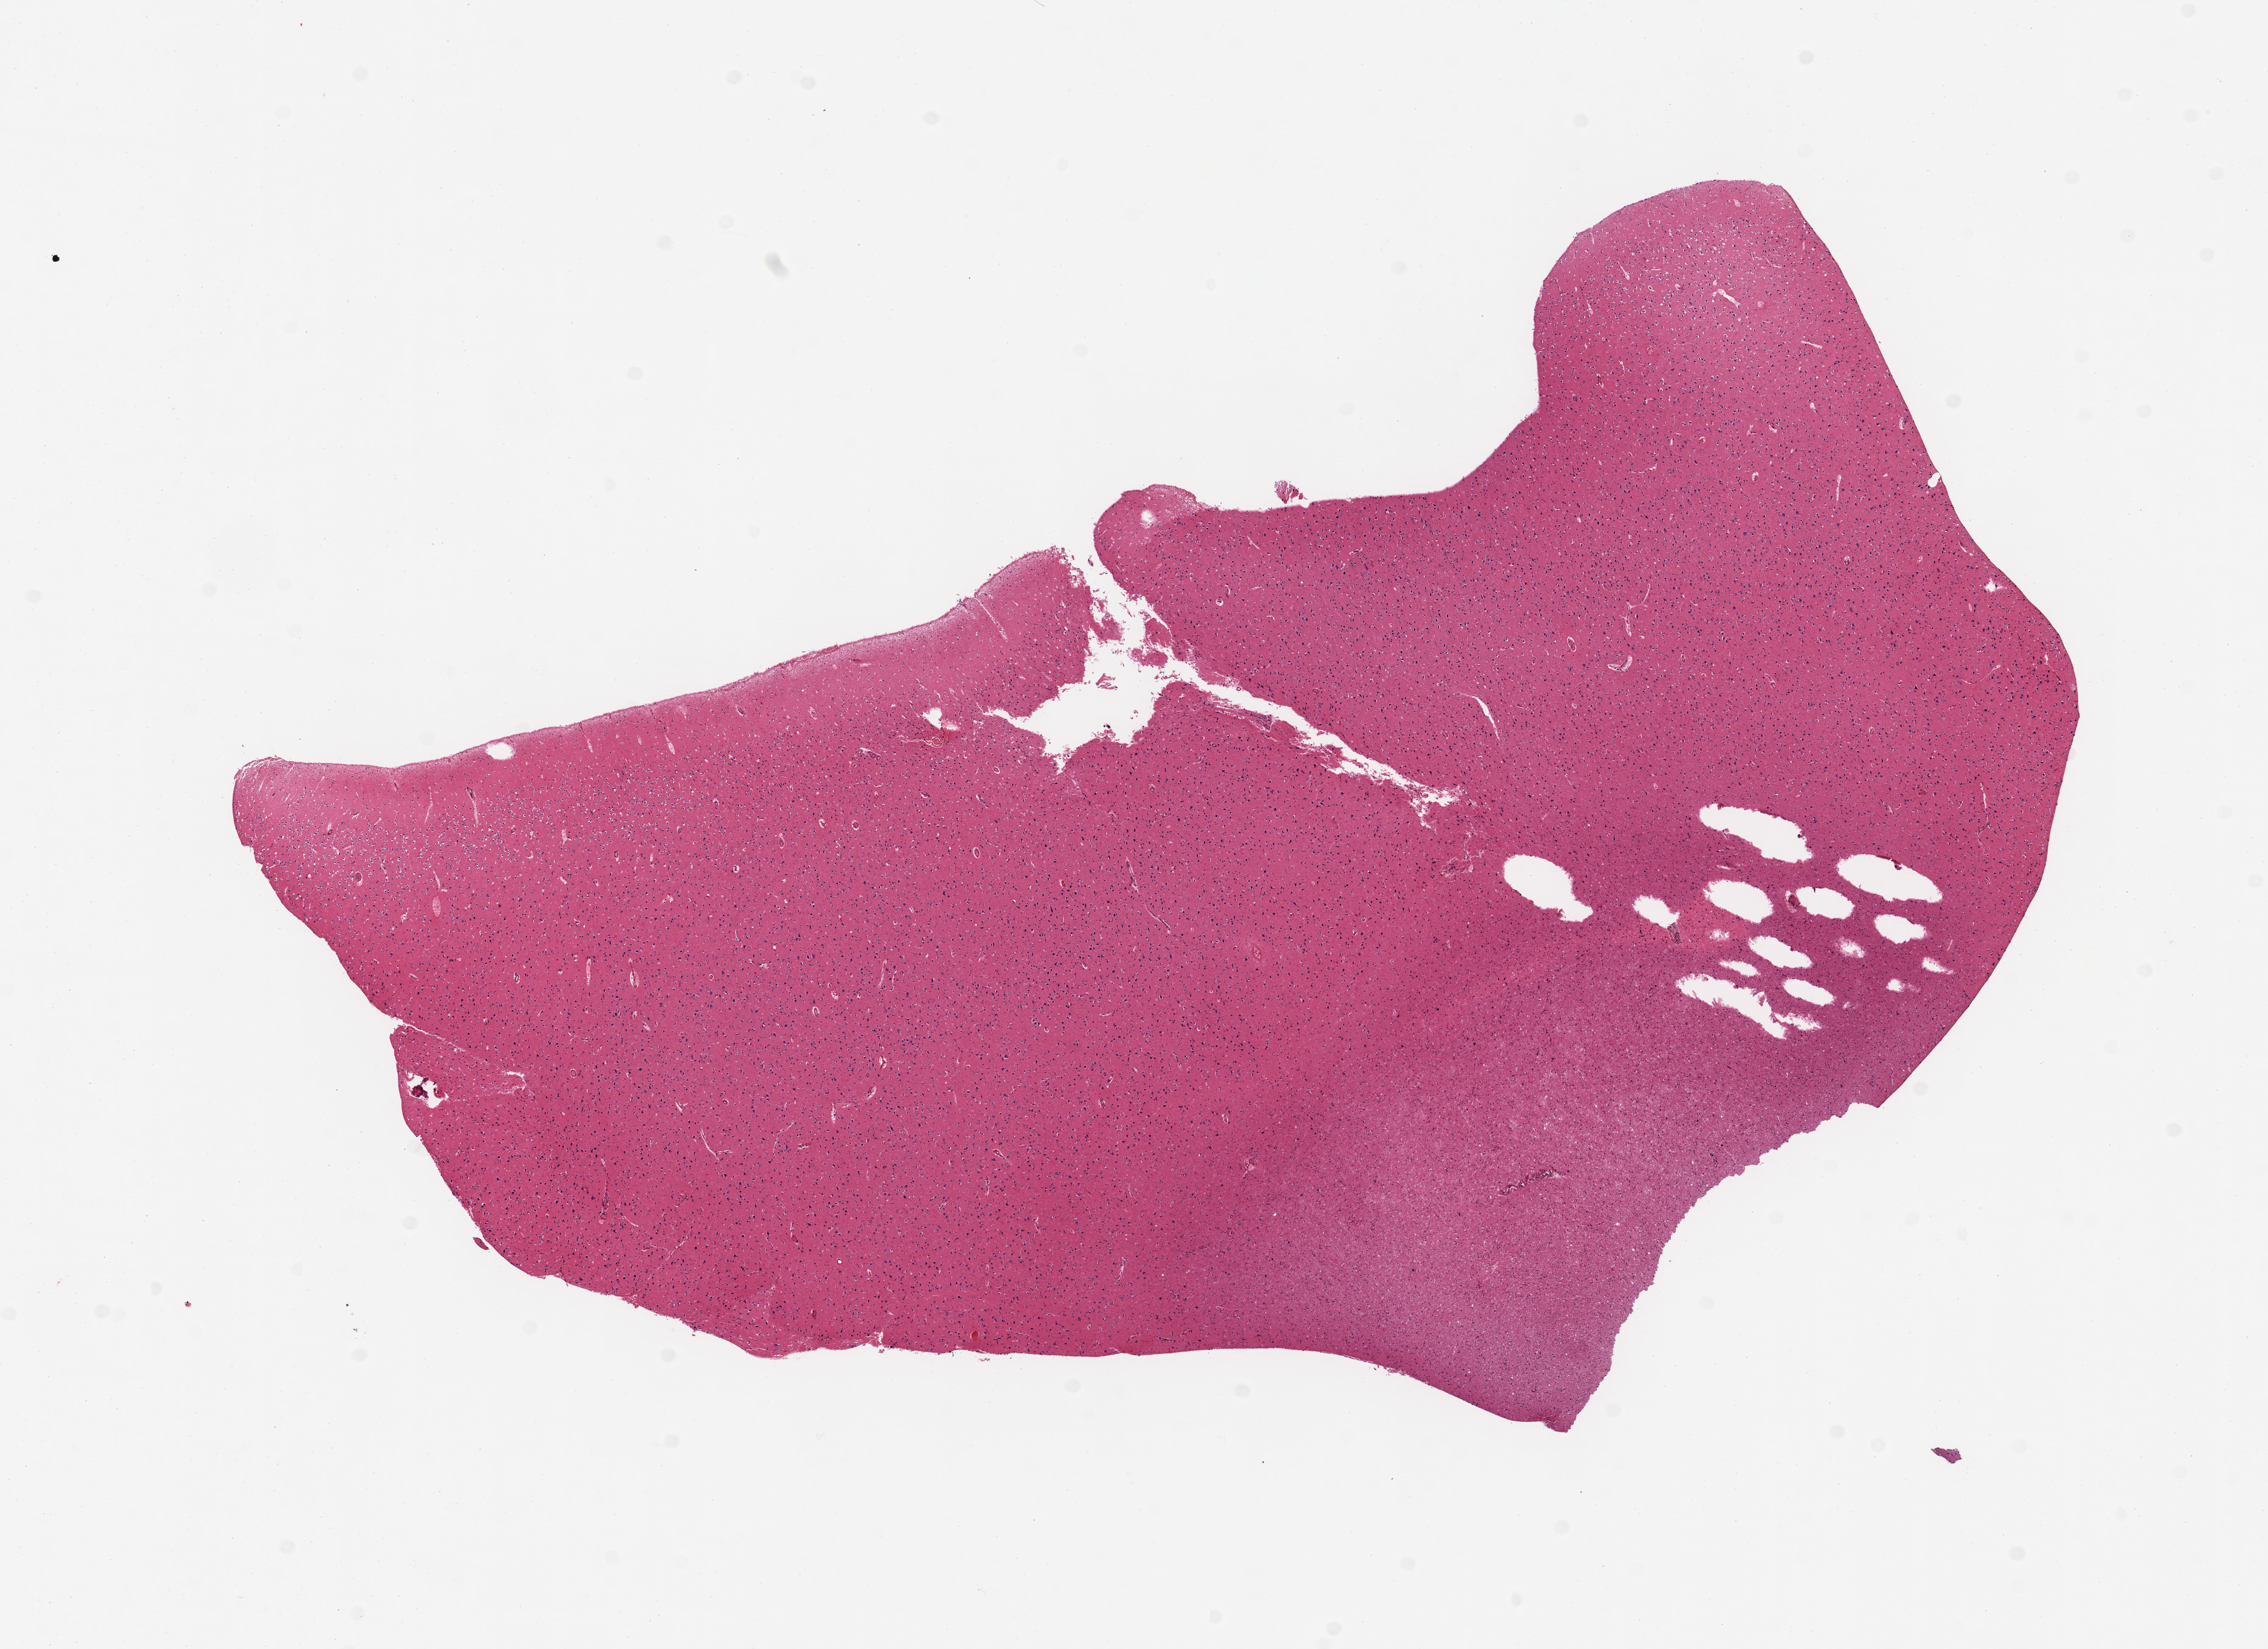
Digitized haematoxylin and eosin-stained section, whole scanned area (about 14.8 x 10.7 mm, from a 20x scan) shown as a low-resolution overview. PAXgene-fixed, paraffin-embedded tissue. Target tissue: cerebral cortex. Tissue donor sample. Donor: female.
Pathologist's review note for this sample: 1 piece.